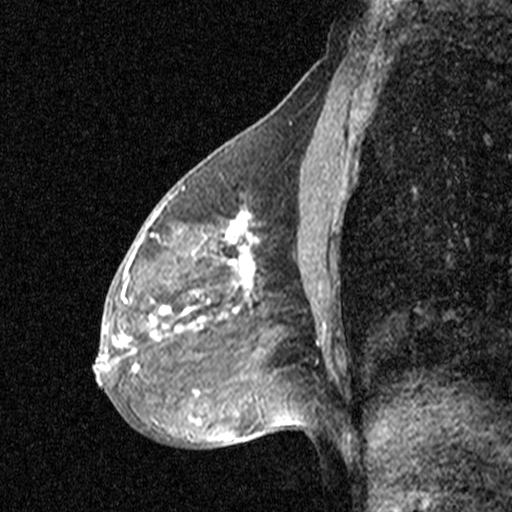
Breast MRI (dynamic contrast-enhanced), one sagittal slice; slice 23 of 44 in the series (ordered by position); dynamic contrast-enhanced study with each time point stored as its own series, time point 2 of 3 at this slice position (early post-contrast, ordered by acquisition time); 1.5 T; TE 4.5 ms, TR 11 ms; 3 mm slice thickness; 512 × 512 image matrix, field of view 200 × 200 mm. Female patient, age 53 years. From the clinical record (not read from this slice): setting: breast cancer imaged before/during neoadjuvant chemotherapy; receptor status: HR-positive, HER2-negative.
Annotated regions visible in this slice (semi-automatically segmented with operator editing):
- analysis volume of interest (the breast-tissue region the enhancement analysis was run in; not a lesion): box from (x=88, y=176) to (x=313, y=423) px
- tumour enhancement mask (voxels above the 90 % enhancement threshold inside the analysis volume of interest): (x=95, y=198)–(x=254, y=384)